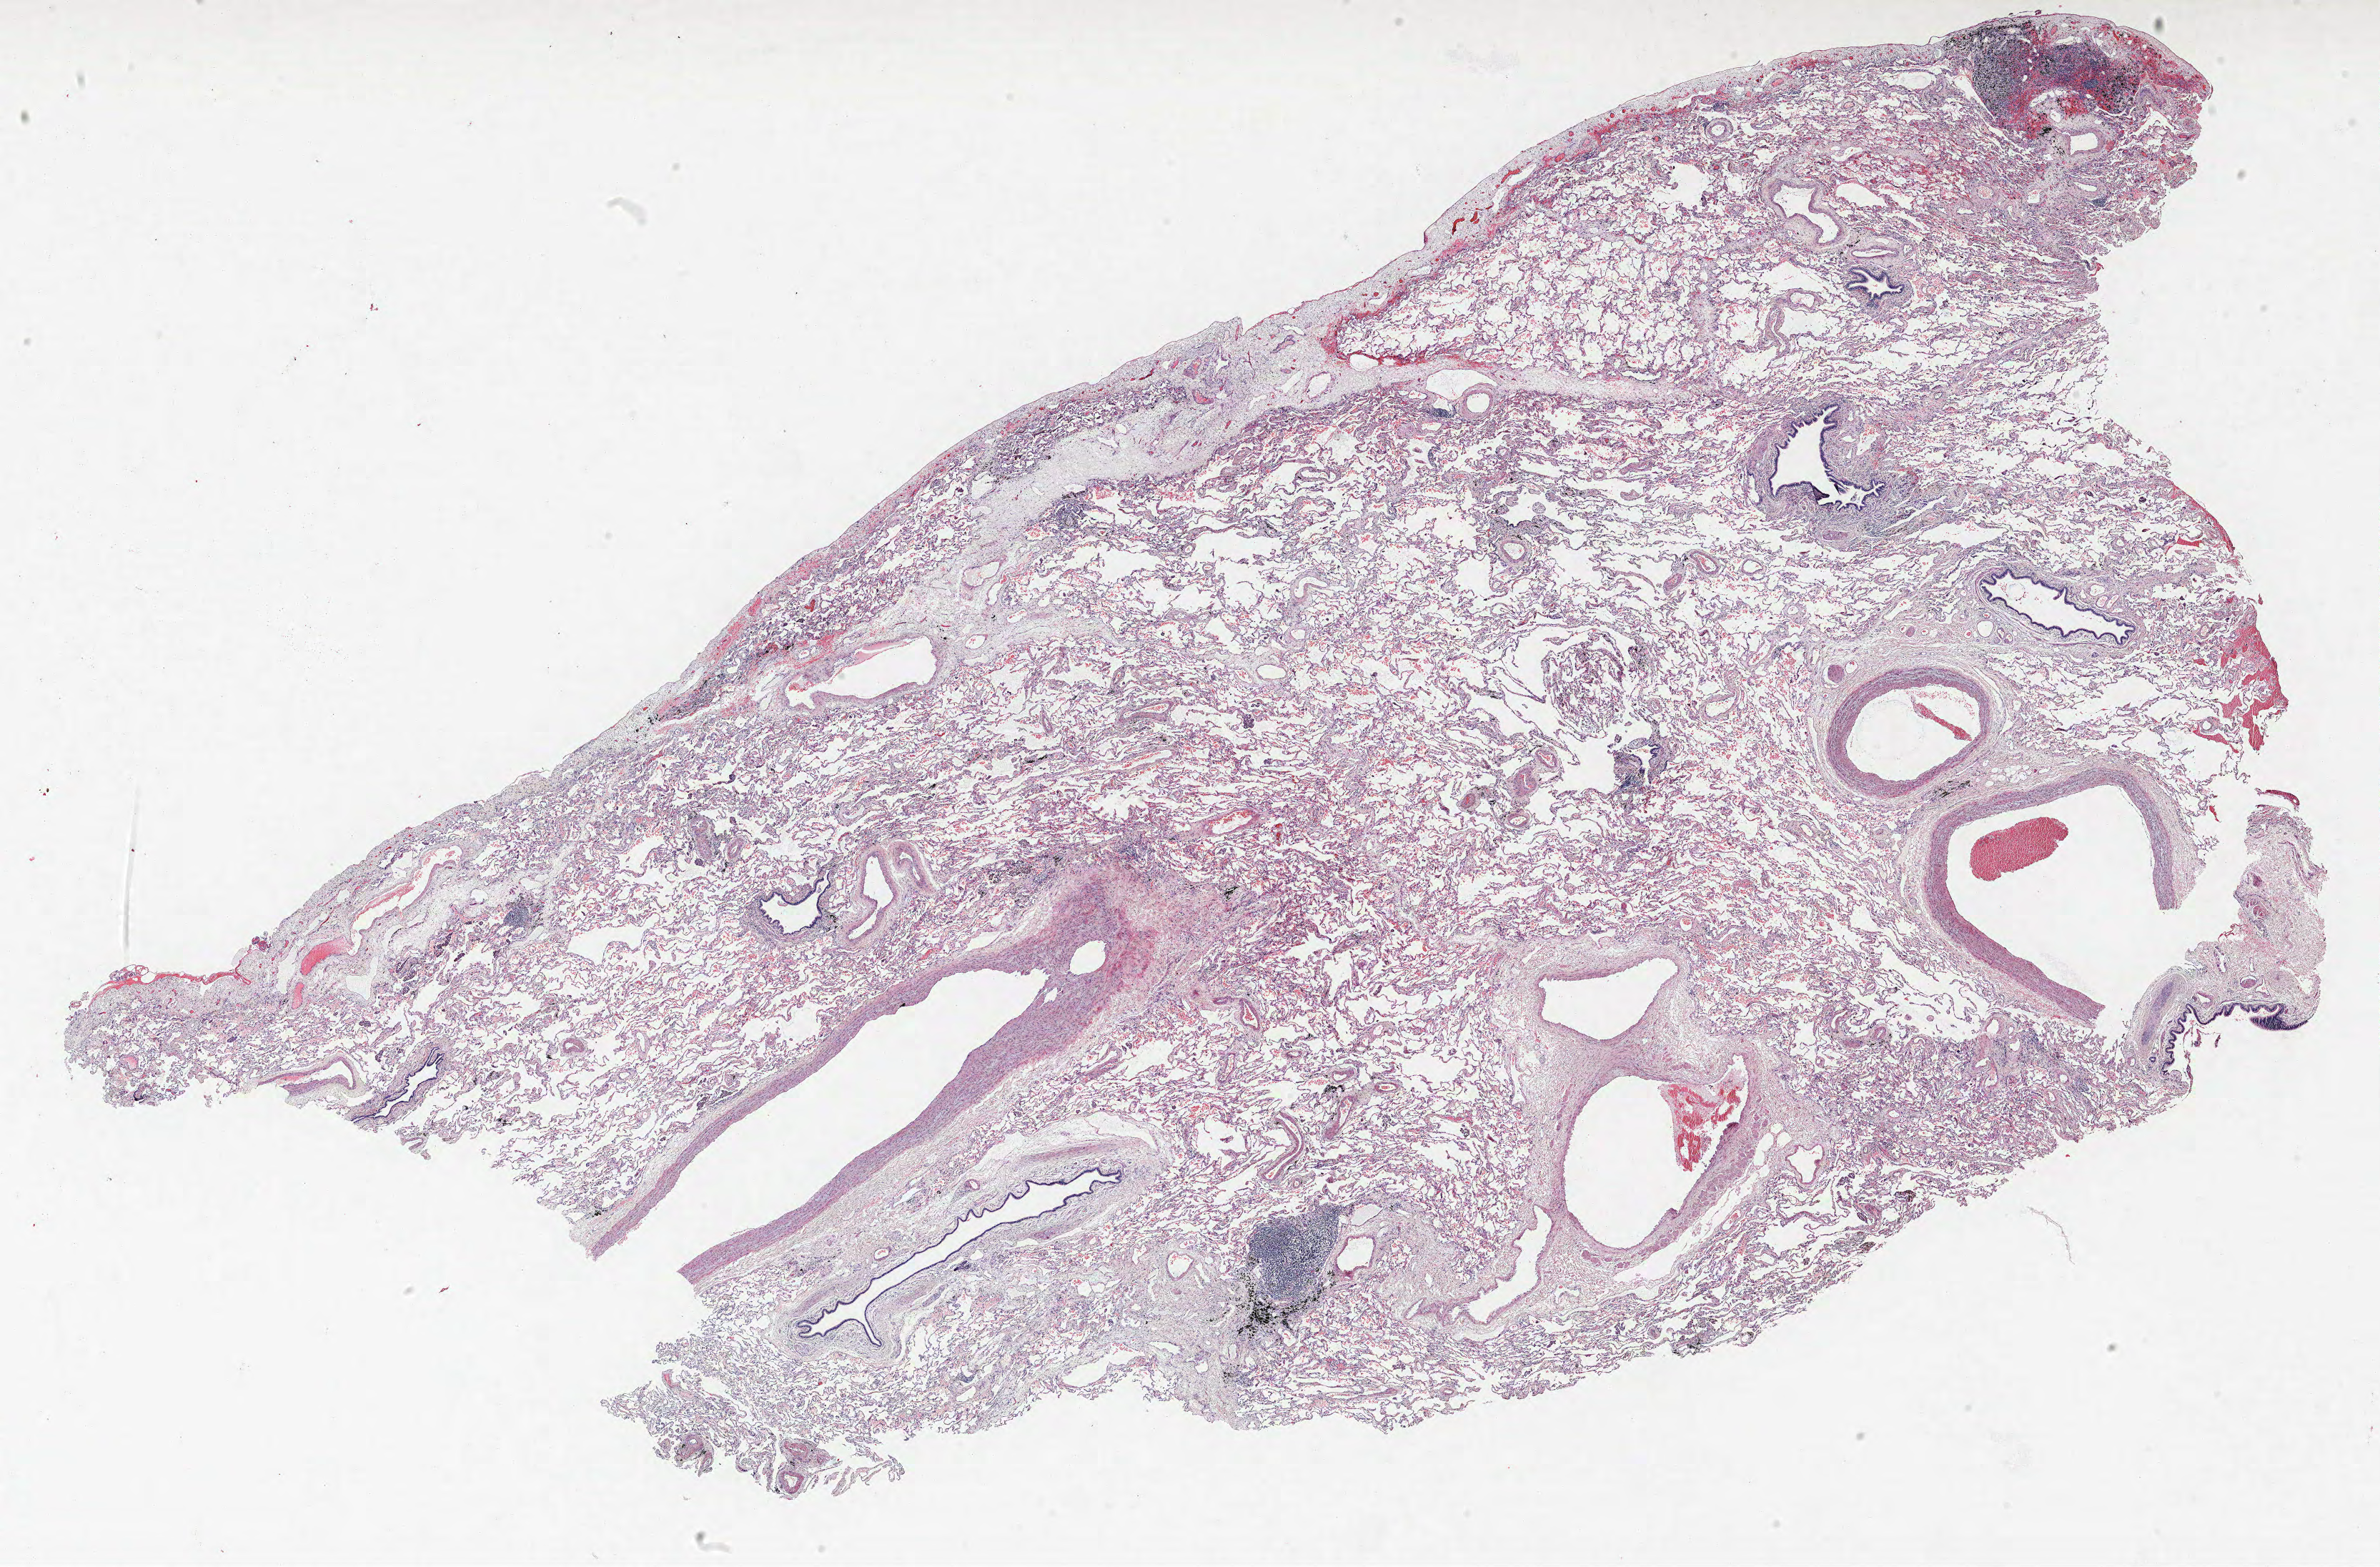
H&E-stained whole-slide image, a low-resolution overview of the entire scanned area, about 26.6 x 17.5 mm (from a 40x scan). Formalin-fixed paraffin-embedded (FFPE) section. Lung tissue. Female, age 61 at enrolment. Grade: poorly differentiated (G3).
Primary tumour location (clinical record): left upper lobe. Stage (AJCC 6th edition): IB. Tumour size (pathology): 30 mm. Participant's lung-cancer diagnosis: Squamous cell carcinoma, NOS.